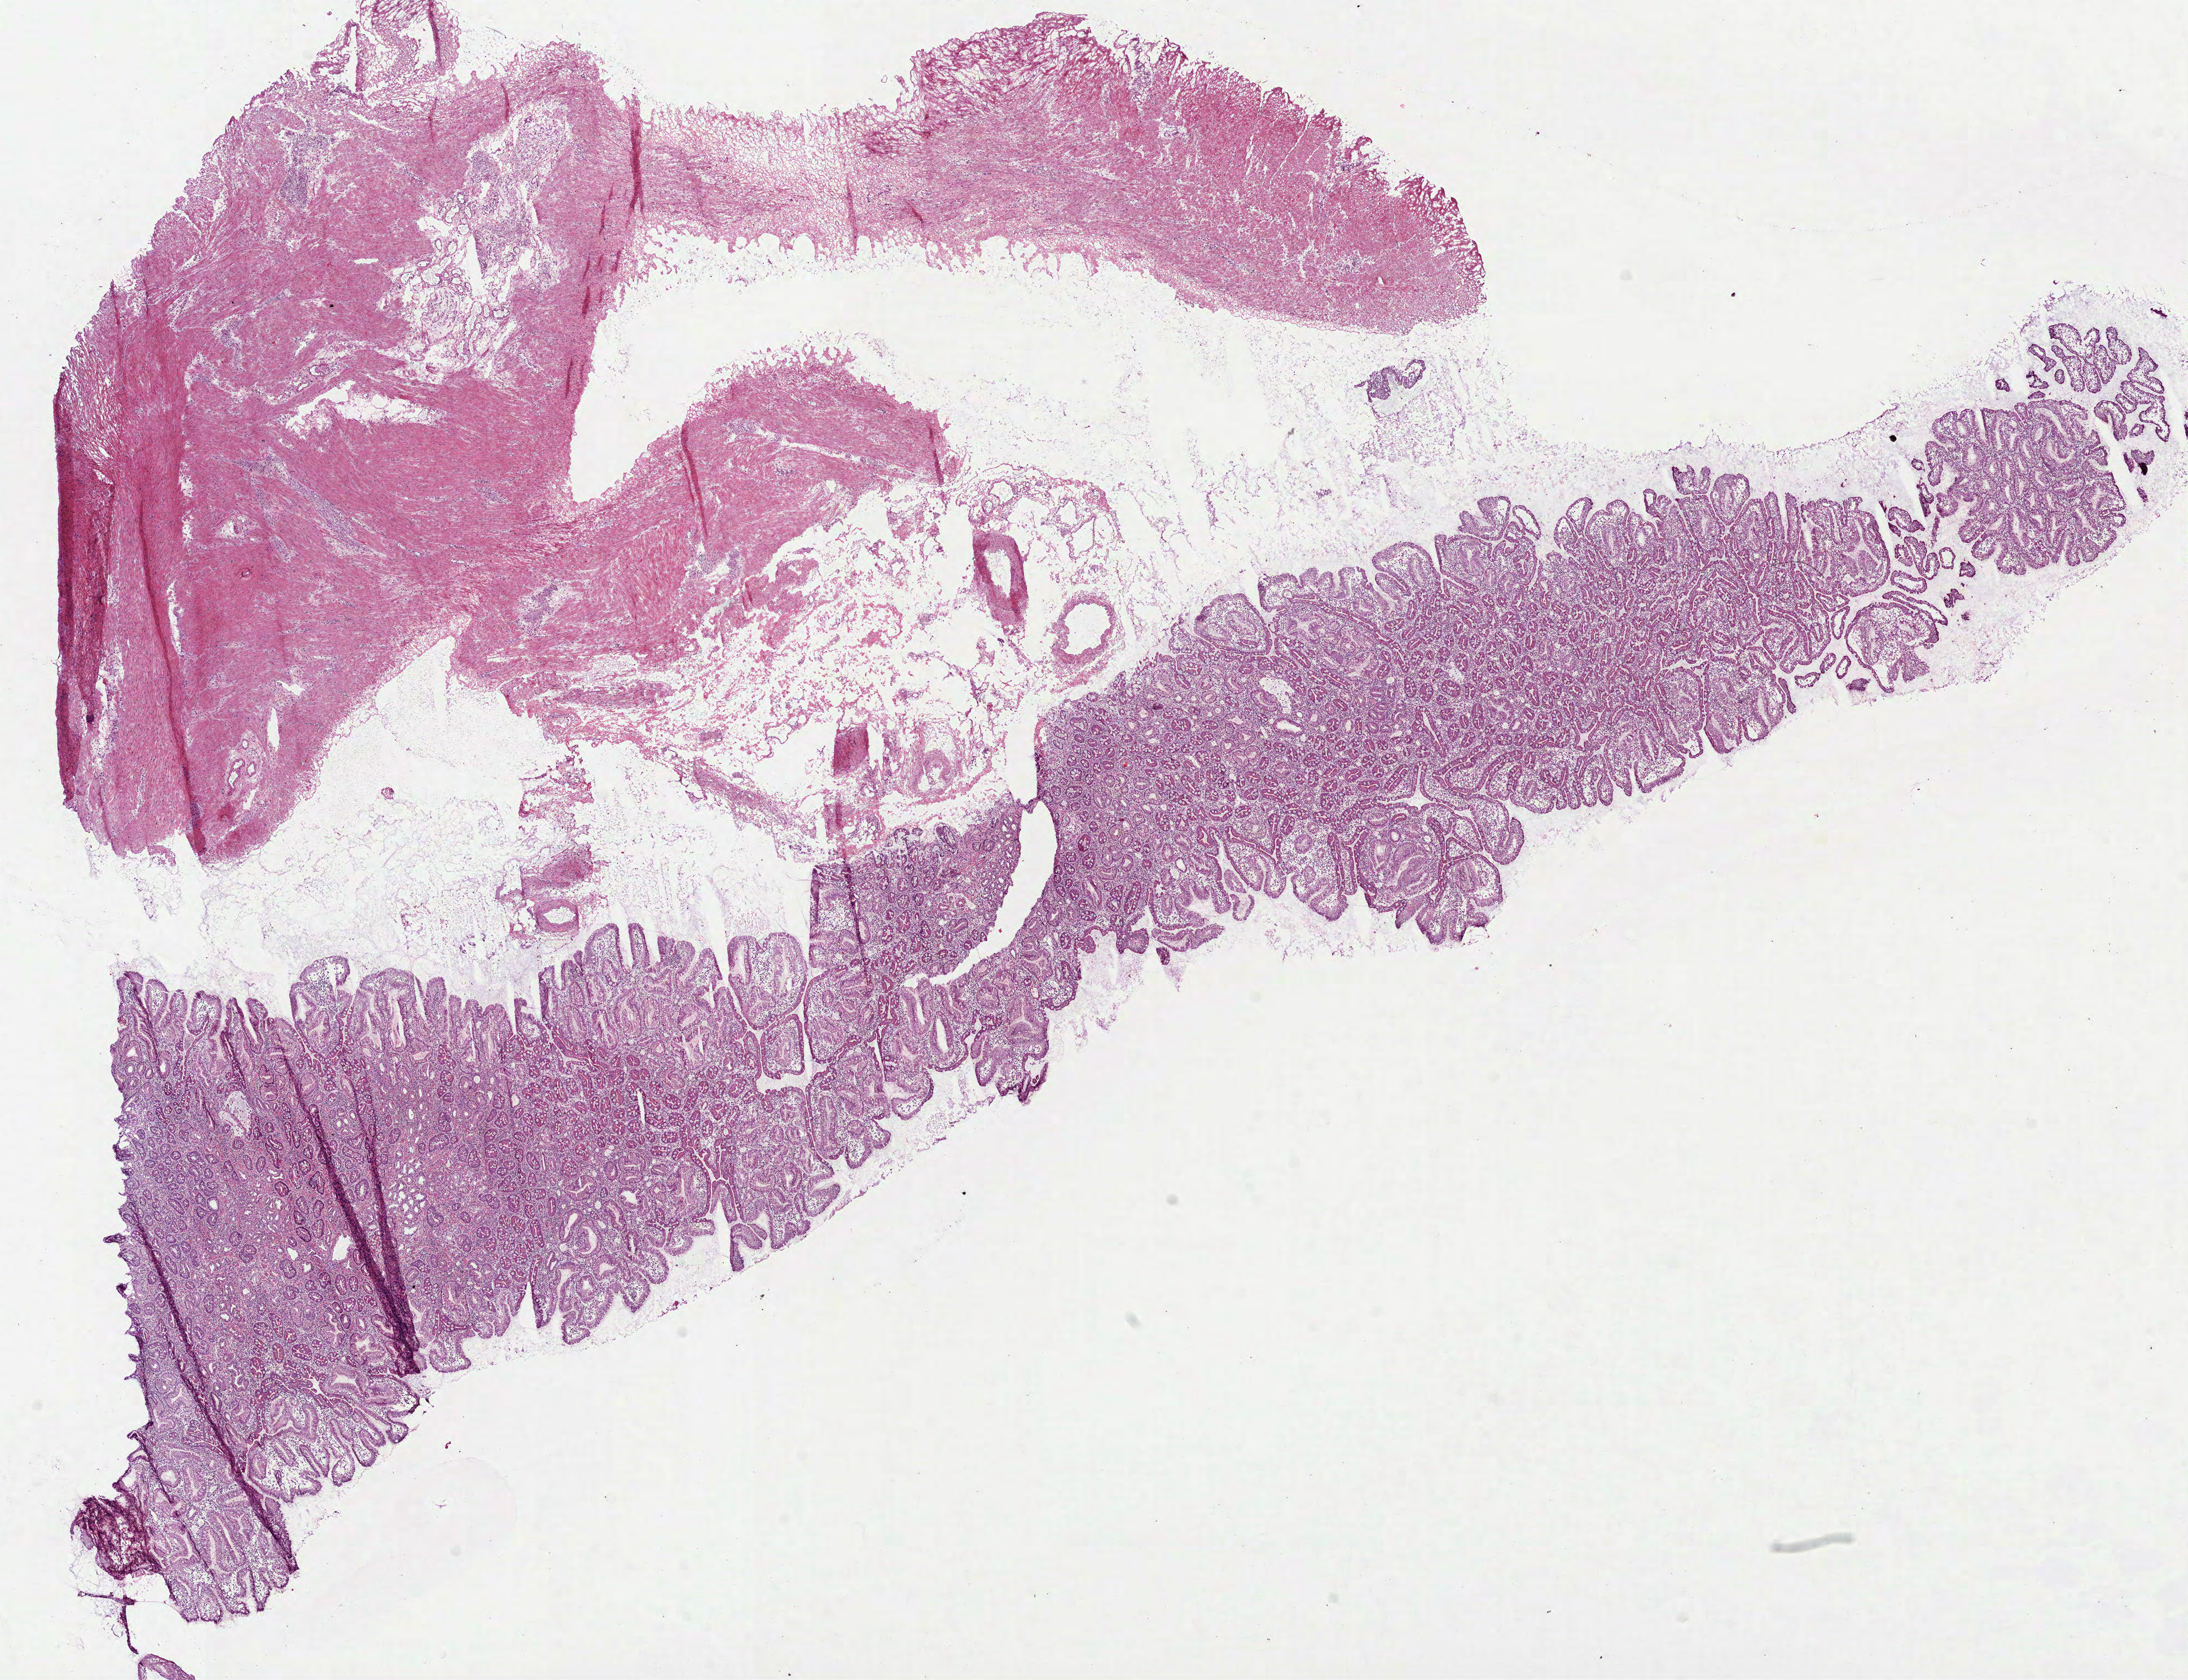
Hematoxylin and eosin (H&E) stained whole-slide image — whole scanned area (about 16.1 x 12.3 mm, from a 40x scan) shown as a low-resolution overview; frozen section from the top of the tissue portion; solid tissue normal (non-tumour tissue) sample from the stomach. Male, age 69 years at initial diagnosis.
- this section: solid tissue normal sample (biorepository sample class)
- patient diagnosis: Adenocarcinoma, NOS (body of stomach)